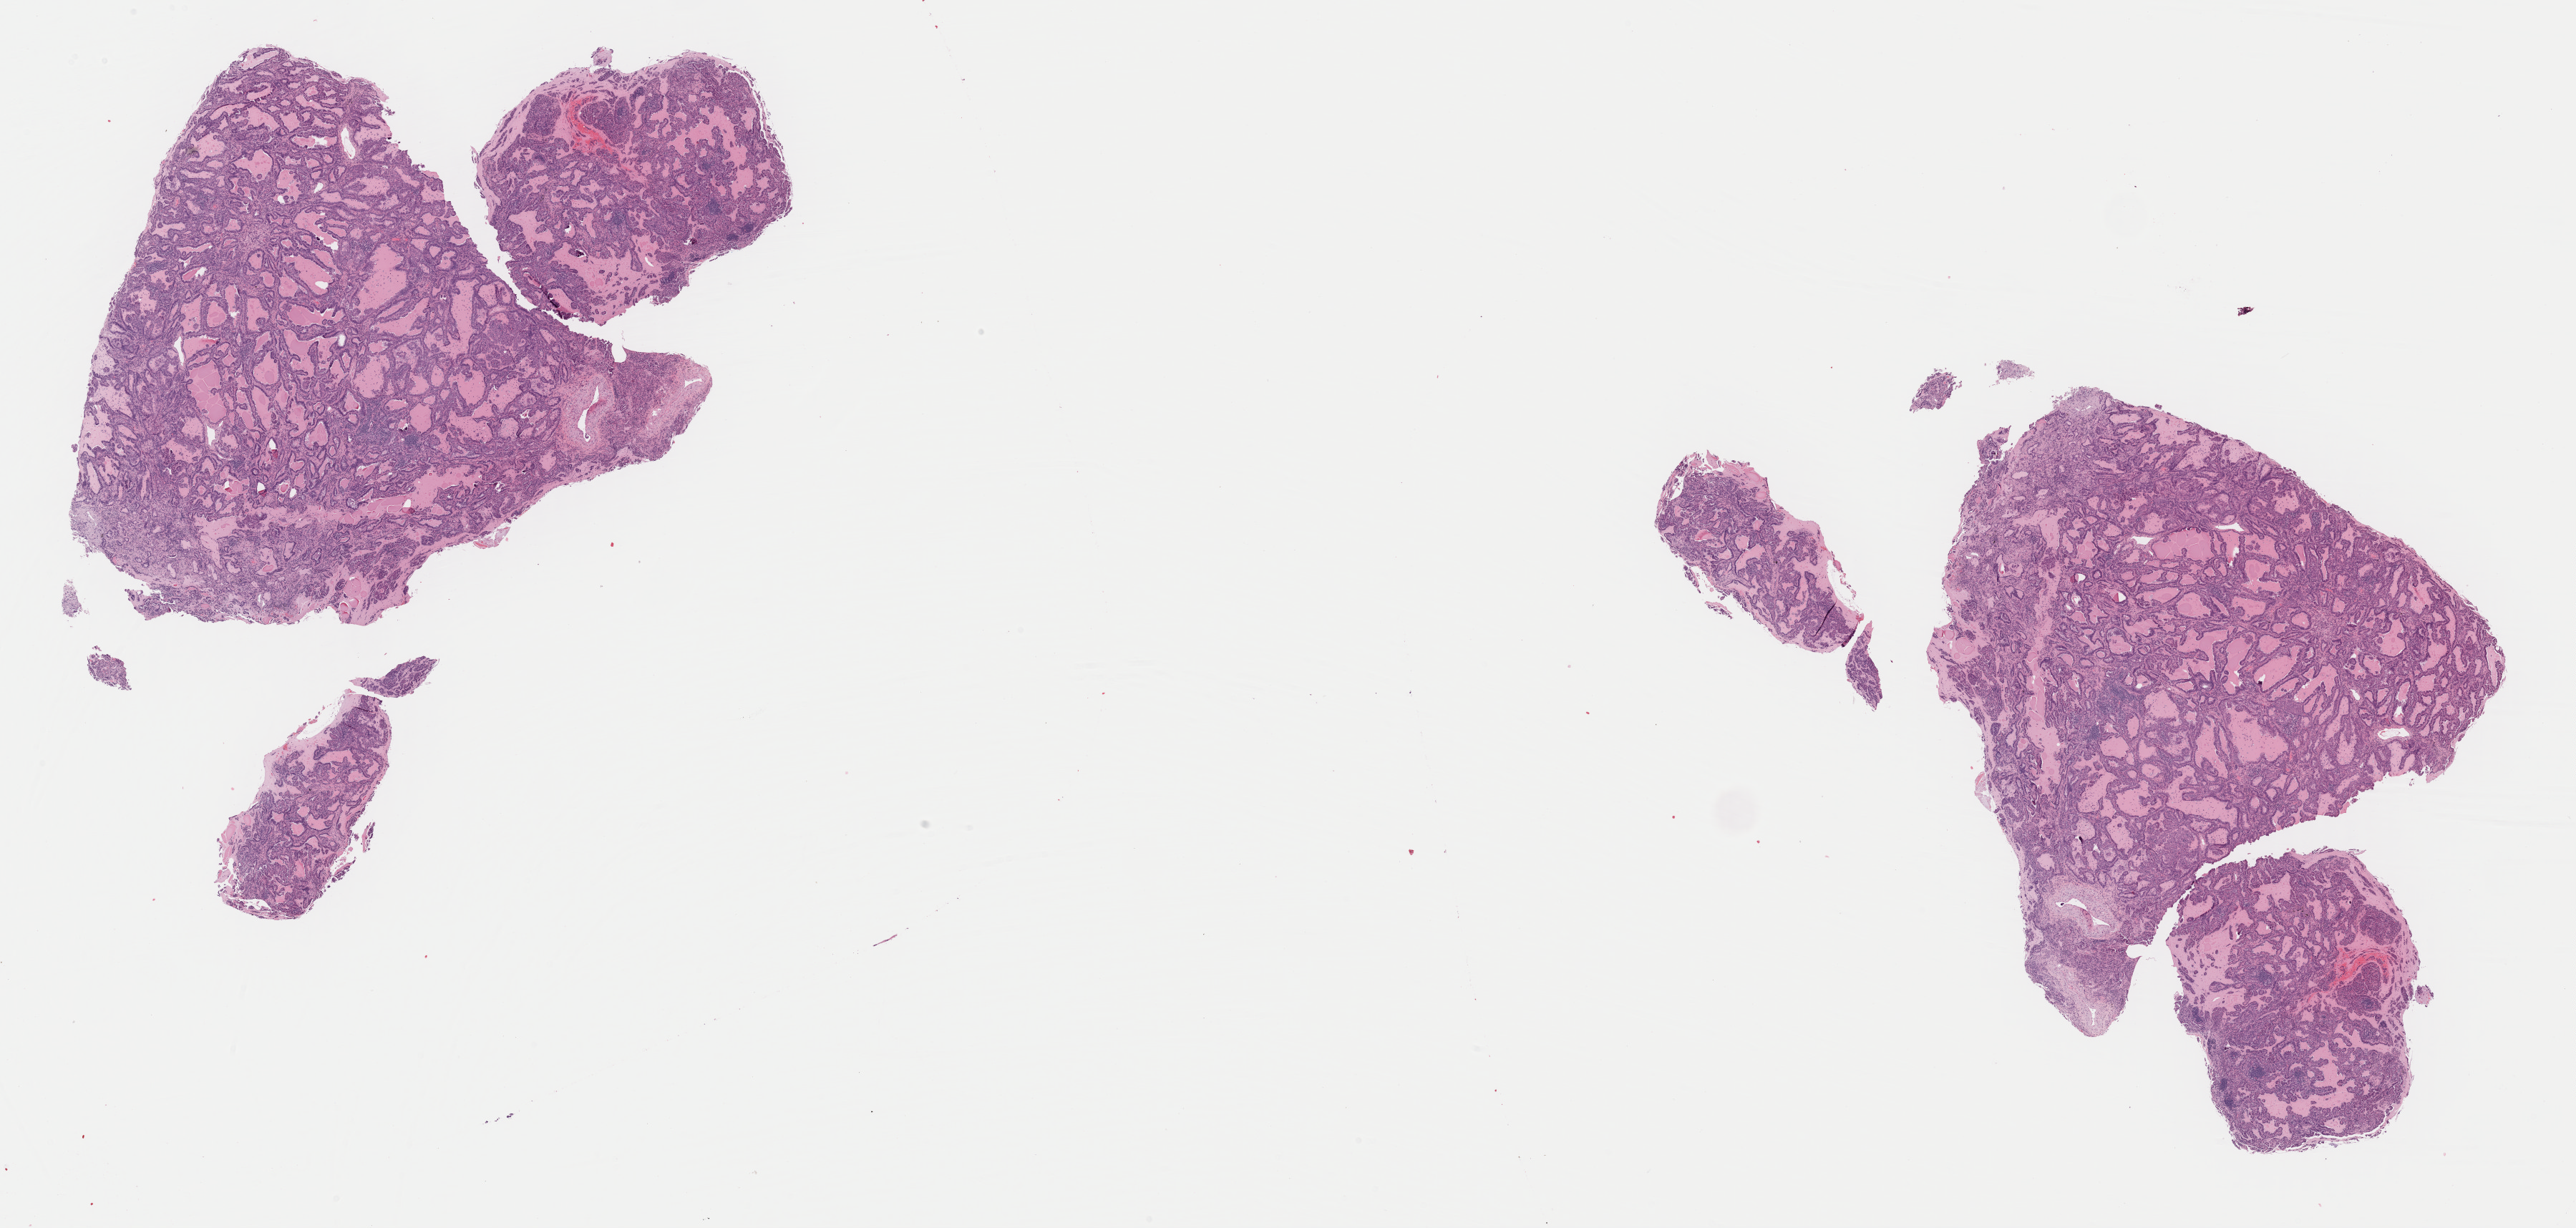
Digitized H&E-stained tissue section (whole slide), shown as a low-resolution overview of the whole scanned area (about 28.4 x 13.6 mm, acquisition: 40x scan); formalin-fixed paraffin-embedded (FFPE) diagnostic section; lung, primary tumour sample. Male, age 78 years at initial diagnosis.
Laterality: left. AJCC pathologic stage: IIA. Histologic diagnosis: Adenocarcinoma, NOS (lower lobe, lung).